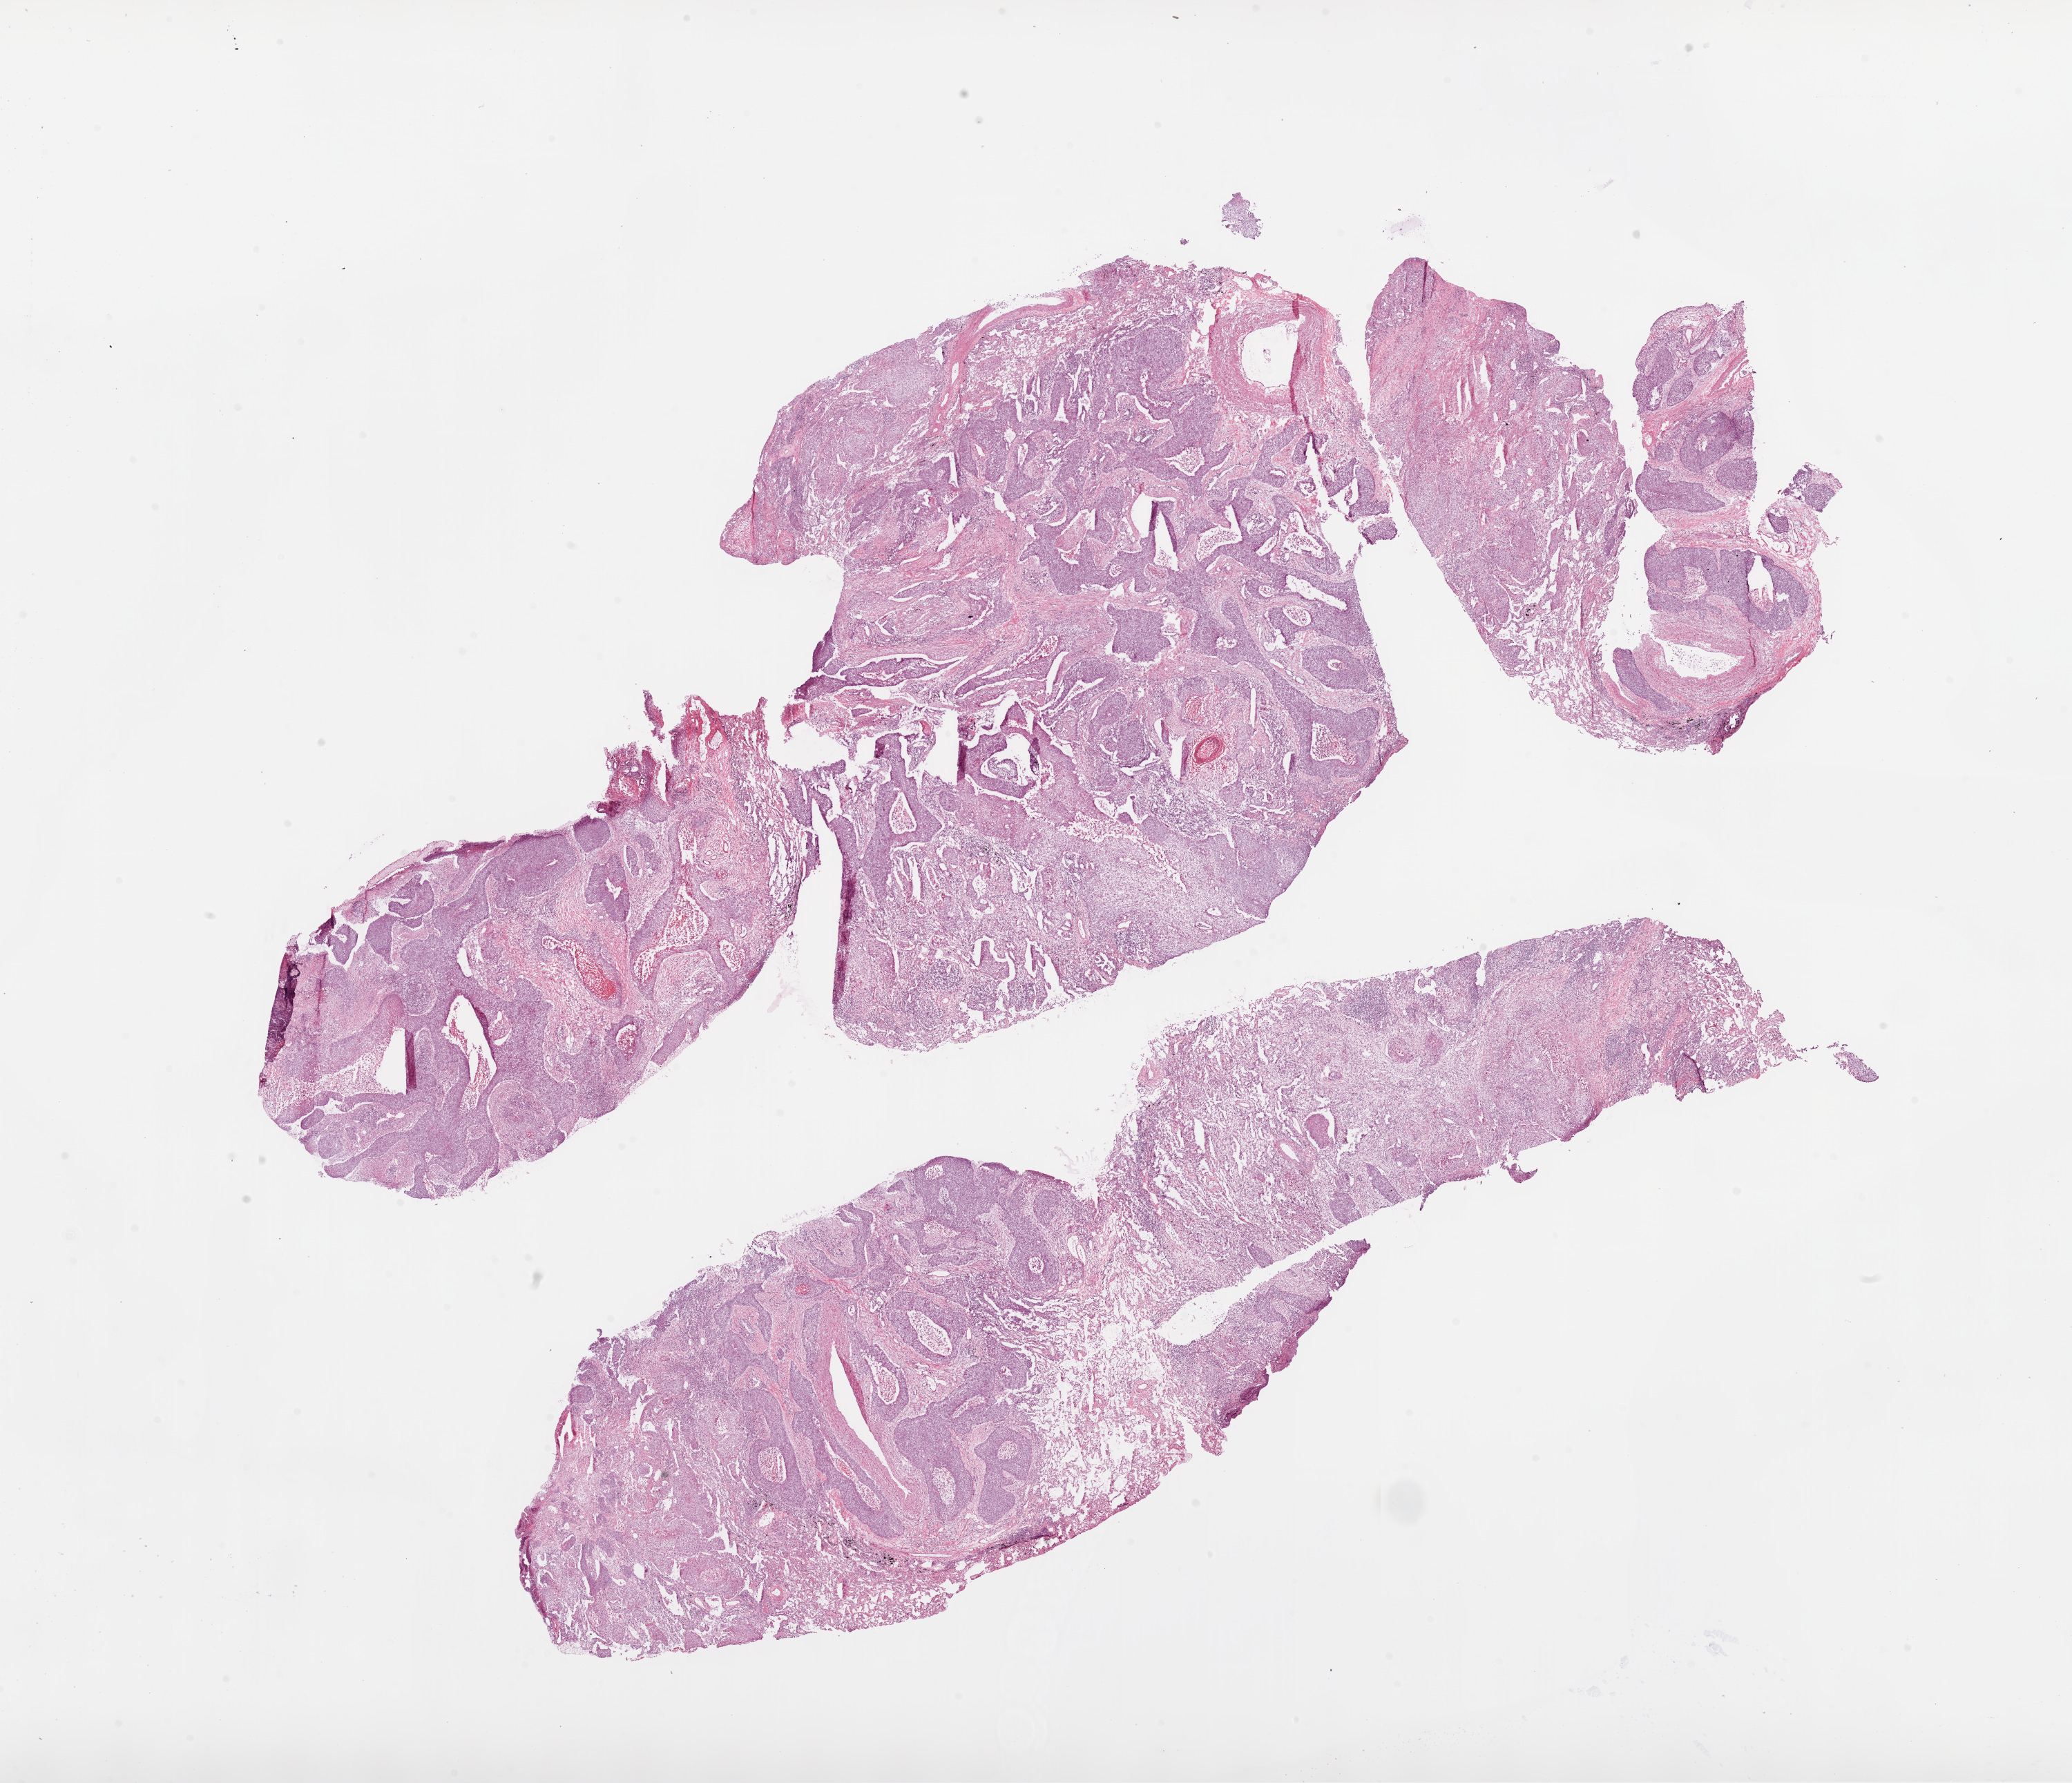
H&E-stained whole-slide image, a low-resolution overview of the entire scanned area, about 24.1 x 20.7 mm (slide scanned at 20x), frozen section, sample: primary tumour, lung. Female, age 76 years at initial diagnosis. Composition of this section per pathologist review: tumour cells 60%, tumour nuclei 65%, normal cells 10%, stromal cells 20%, necrosis 10%.
Pathologic diagnosis: Squamous cell carcinoma, NOS (upper lobe, lung). AJCC pathologic stage: IA (6th edition).